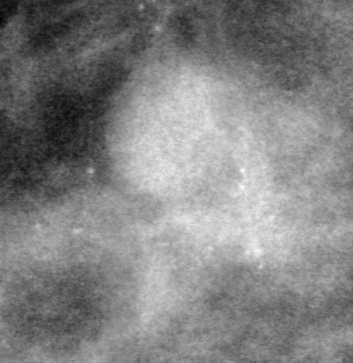
Crop from a digitized film mammogram around one marked abnormality, right breast, CC view, BI-RADS breast density category 2 (scale 1–4).
- Marked abnormality: mass, shape round, margins obscured; BI-RADS assessment category 0 (incomplete: needs additional imaging); pathology result (as recorded, not read from the image): benign.